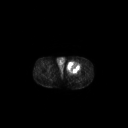
FDG PET of an extremity soft-tissue mass (from a PET/CT study), one axial slice; position 258 of 267 along the scan axis; 3.27 mm slice thickness; 128 × 128 image matrix, field of view 700 × 700 mm. Patient: male, 63 years. Case-level facts recorded for this patient, not image findings: histological type: pleiomorphic liposarcoma; grade: high; site of the primary tumour: left thigh.
Structures marked on this image (expert contour drawn on MRI and transferred to this co-registered scan by the dataset authors):
- gross tumour volume including surrounding oedema: bounding box [x1, y1, x2, y2] px = [67, 60, 81, 72]
- gross tumour volume (mass): [67, 62, 80, 72]